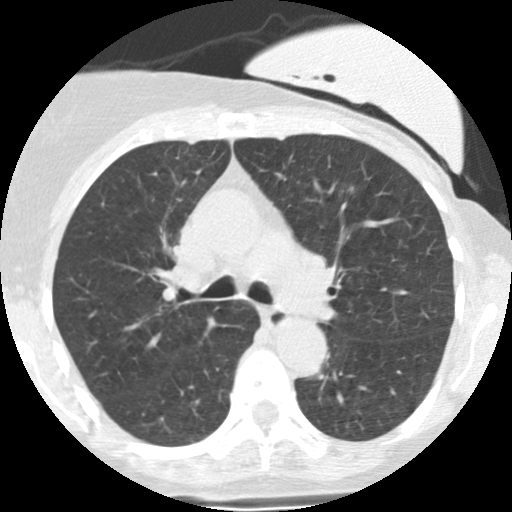
Low-dose screening chest CT, one axial slice; slice 161 of 251 in the series (ordered by position); 120 kVp; lung window (W 1500 / L -600 HU); 512 × 512 image matrix, field of view 280 × 280 mm.
Structures marked on this image (expert manual segmentation):
- lesion 1 (tumor, lower lobe of left lung): bounding box (x1, y1, x2, y2) in pixels: (350, 187, 353, 191)